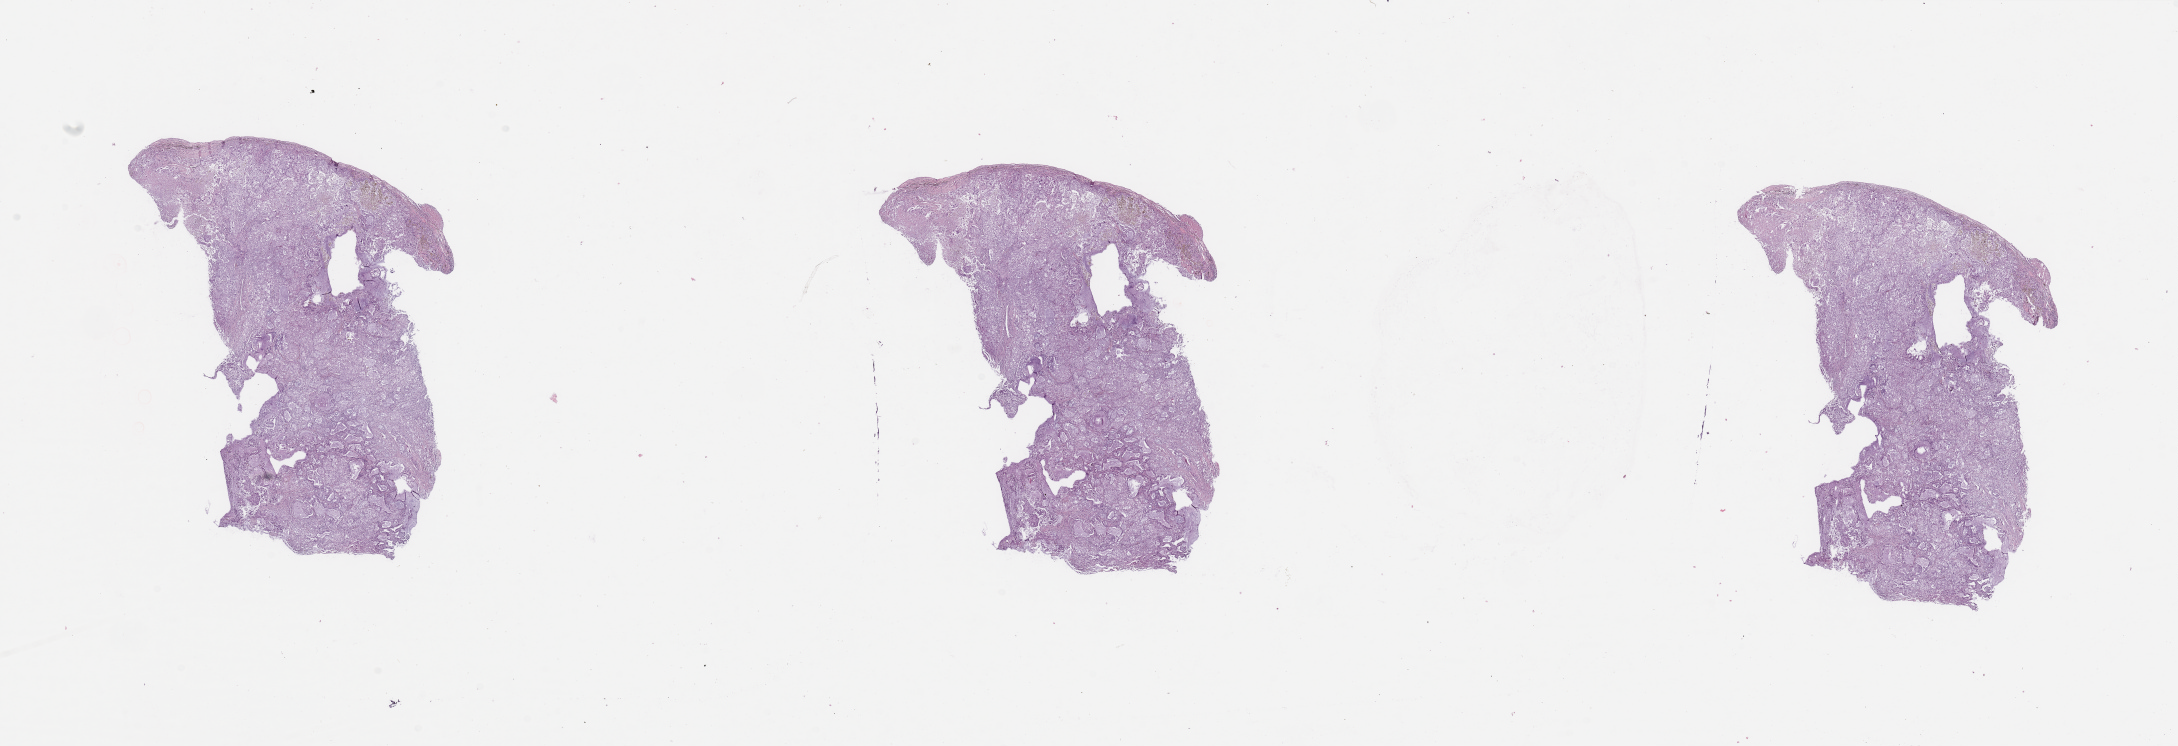
Whole-slide histology image, H&E-stained — shown as a low-resolution overview of the whole scanned area (about 34.5 x 11.8 mm, from a 20x scan). Lung, tumour tissue. Male, 51 y/o. Histologic grade: G2 (moderately differentiated).
• histologic diagnosis: Adenocarcinoma, NOS
• AJCC pathologic stage: IIIA